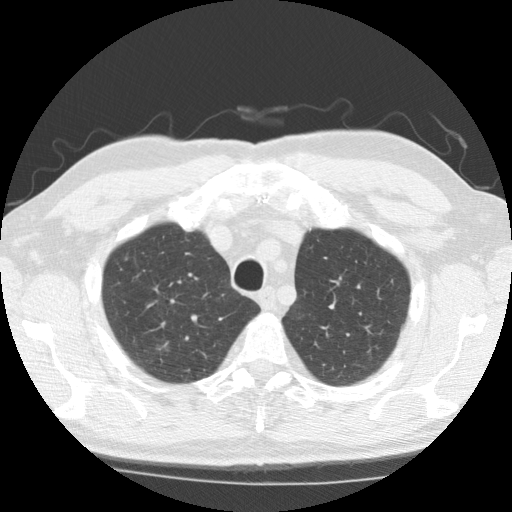
Low-dose screening chest CT, one axial slice; position 157 of 196 along the scan axis; reconstruction kernel STANDARD; 120 kVp; lung window (W 1500 / L -600 HU); 2.5 mm slice thickness; 512 × 512 image matrix, field of view 350 × 350 mm.
Annotated regions visible in this slice (outlined manually by an expert reader):
- lesion 1 (tumor, upper lobe of right lung): bounding box (x1, y1, x2, y2) in pixels: (151, 340, 173, 358)